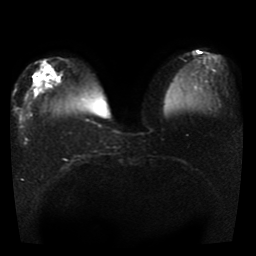
Breast MRI, one axial slice. Diffusion-weighted series; image 2 of 4 stored at this slice position (different b-values; order by instance number). 1.5 T. 5 mm slice thickness. 256 × 256 image matrix. Female patient.
Outlined on this slice (expert manual segmentation):
- tumour on diffusion-weighted imaging: bounding box [x1, y1, x2, y2] px = [34, 70, 47, 86]